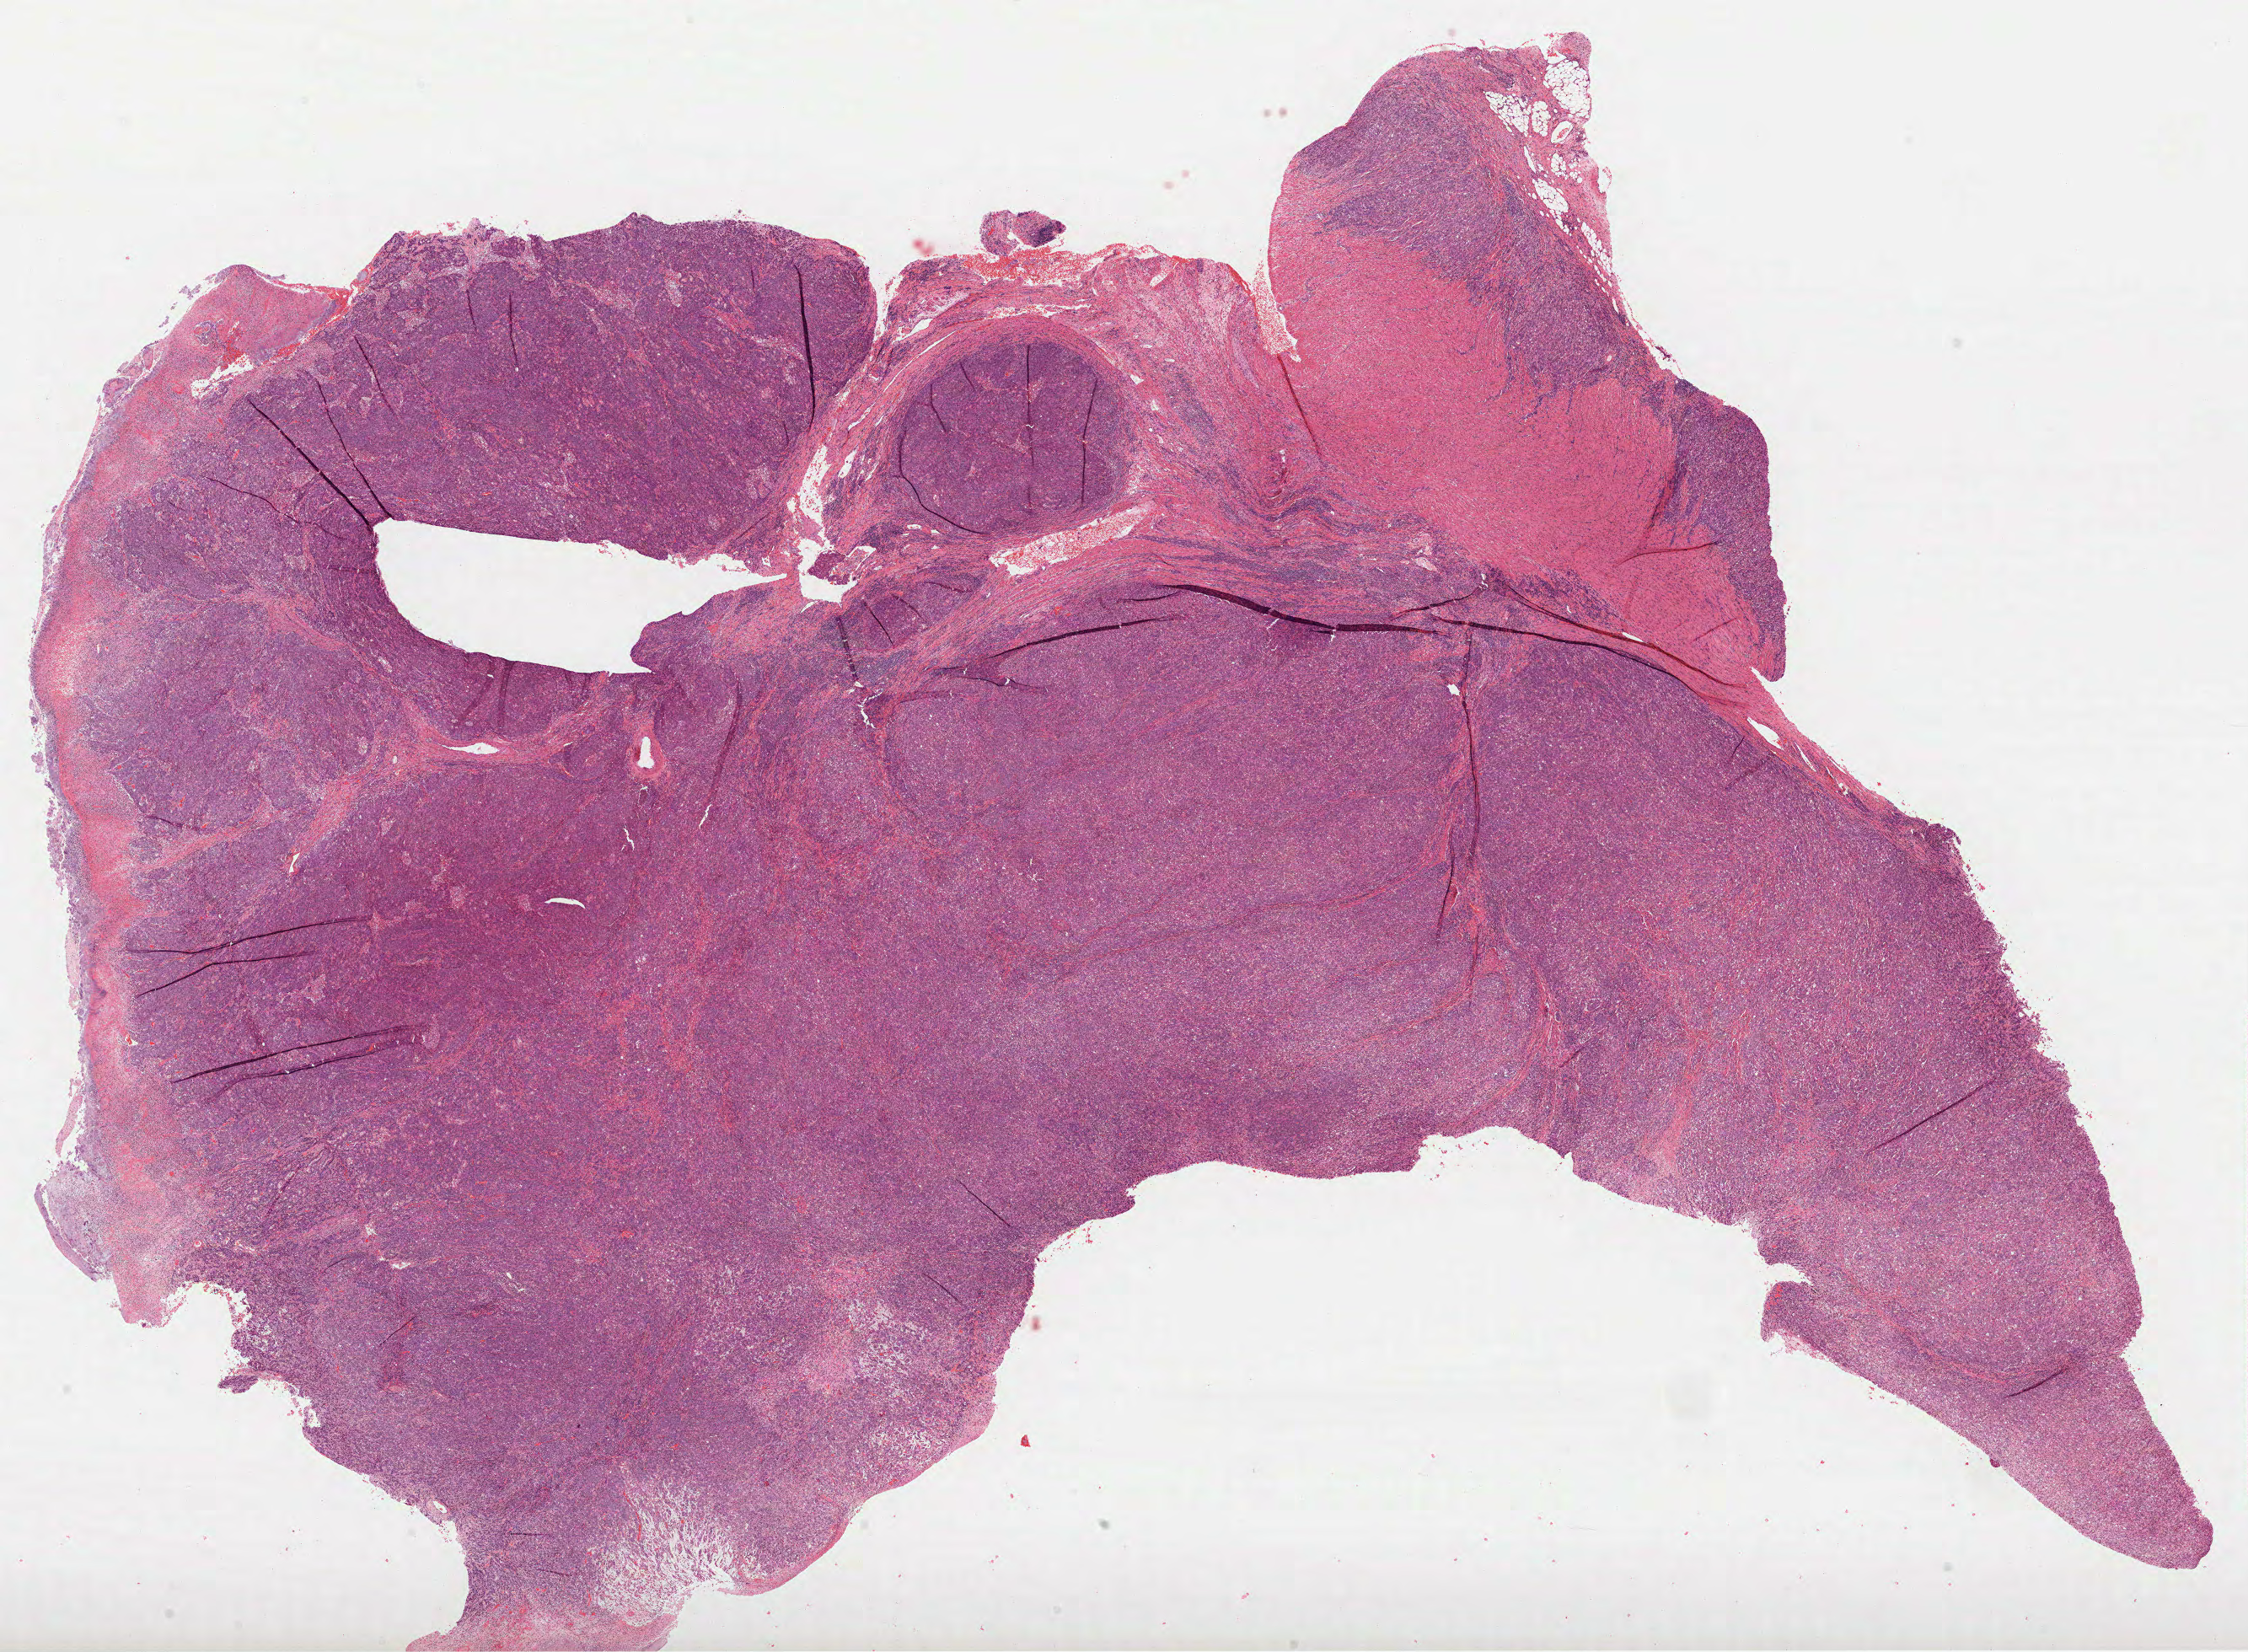
H&E whole-slide image, a low-resolution overview of the entire scanned area, about 21.5 x 15.8 mm, formalin-fixed paraffin-embedded (FFPE) diagnostic section, colon, primary tumour sample. Female patient; age at initial diagnosis 78 years.
Histologic diagnosis: Adenocarcinoma, NOS.